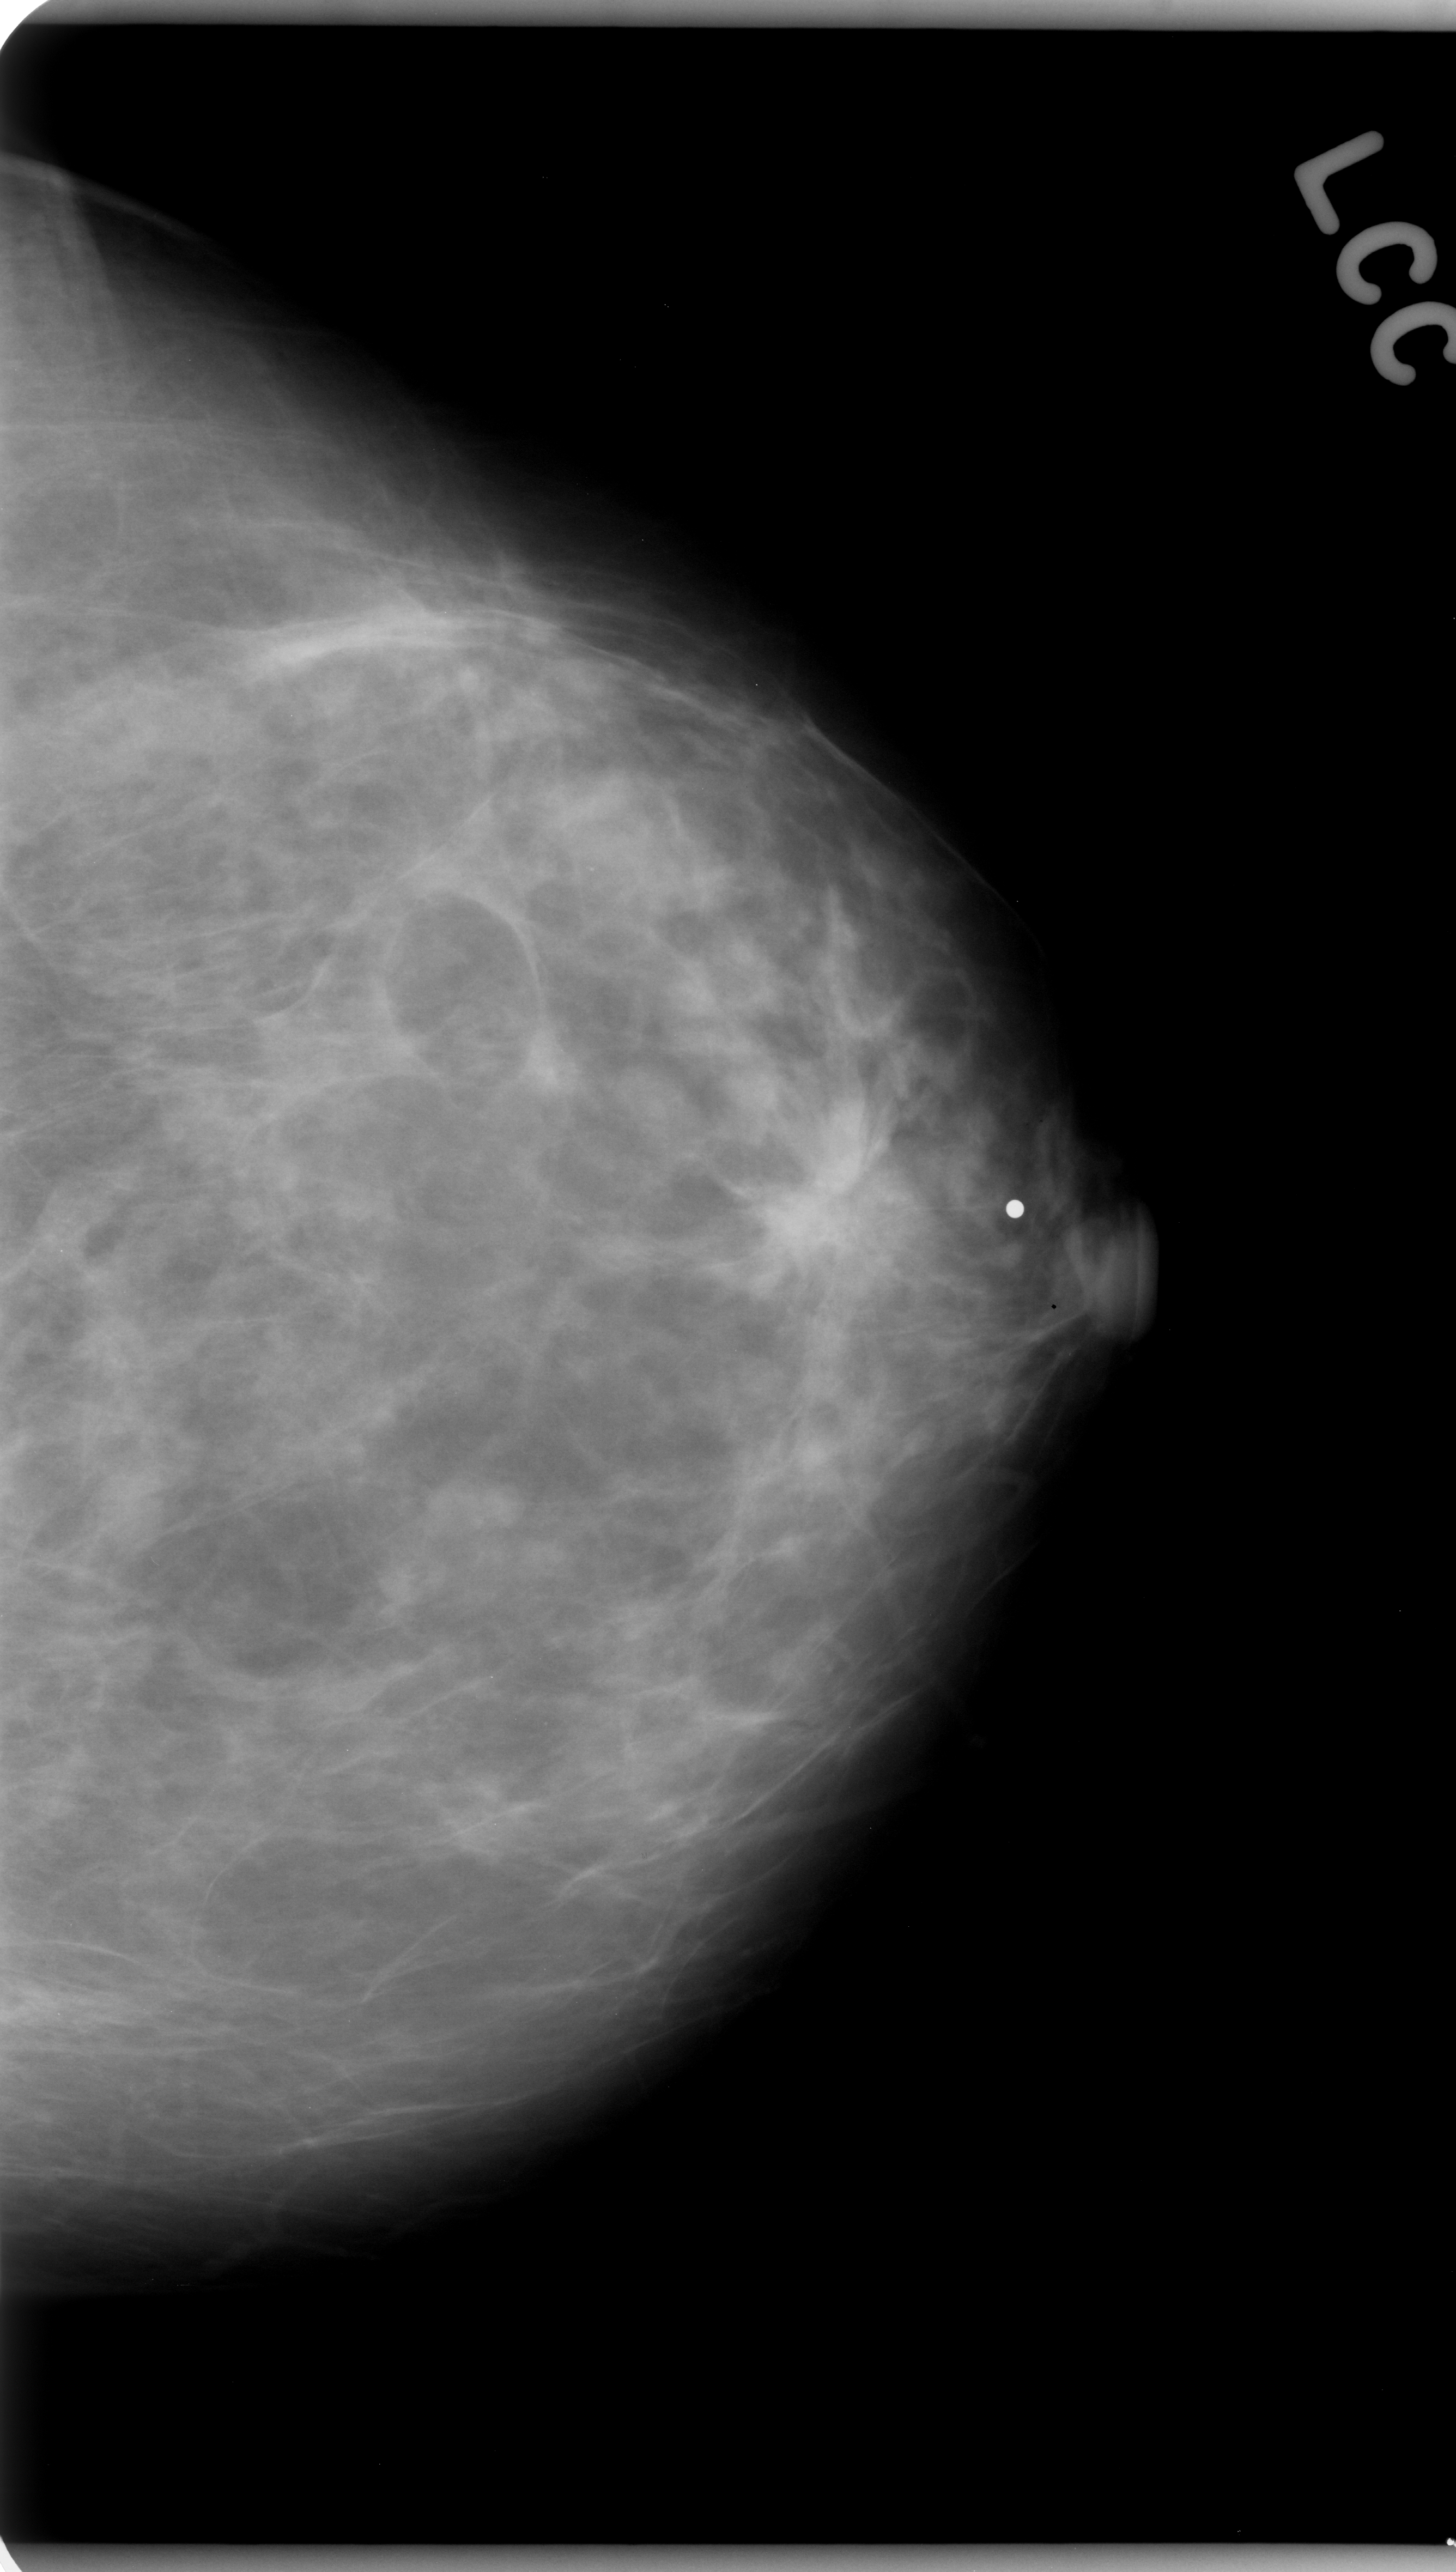
Digitized screen-film mammogram, left breast, craniocaudal (CC) view, breast composition: scattered fibroglandular densities (BI-RADS density category 2 of 4).
- Marked abnormality: mass, shape irregular, margins spiculated; BI-RADS assessment category 5; pathology result (as recorded, not read from the image): malignant.